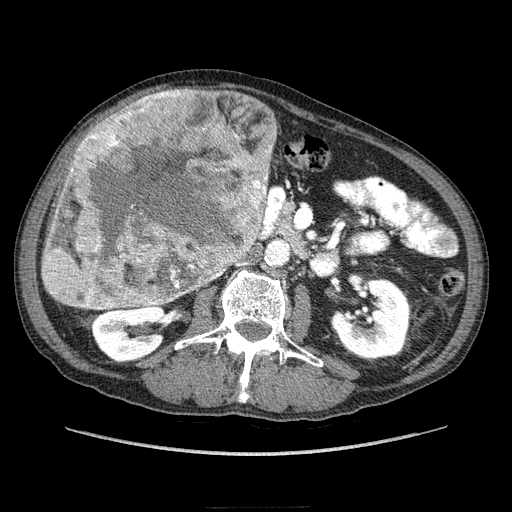
Contrast-enhanced abdominal CT (liver protocol), one axial slice. Position 89 of 218 along the scan axis. Reconstruction kernel STANDARD. 100 kVp. Soft-tissue window (W 400 / L 40 HU). 2.5 mm slice thickness. 512 × 512 image matrix, field of view 380 × 380 mm. From the clinical record (not read from this slice): diagnosis: hepatocellular carcinoma (patient treated with transarterial chemoembolisation; whether this scan precedes or follows treatment is not stated here); TNM stage (as recorded): Stage-IIIA; Child-Pugh class: A; tumour differentiation: well differentiated.
Outlined on this slice (semi-automatically segmented with operator editing):
- liver parenchyma outside the tumour (the mass and vessels are separate outlines, so this box may not span the whole liver): box from (x=82, y=110) to (x=276, y=180) px
- mass: (x=40, y=88)–(x=275, y=312)